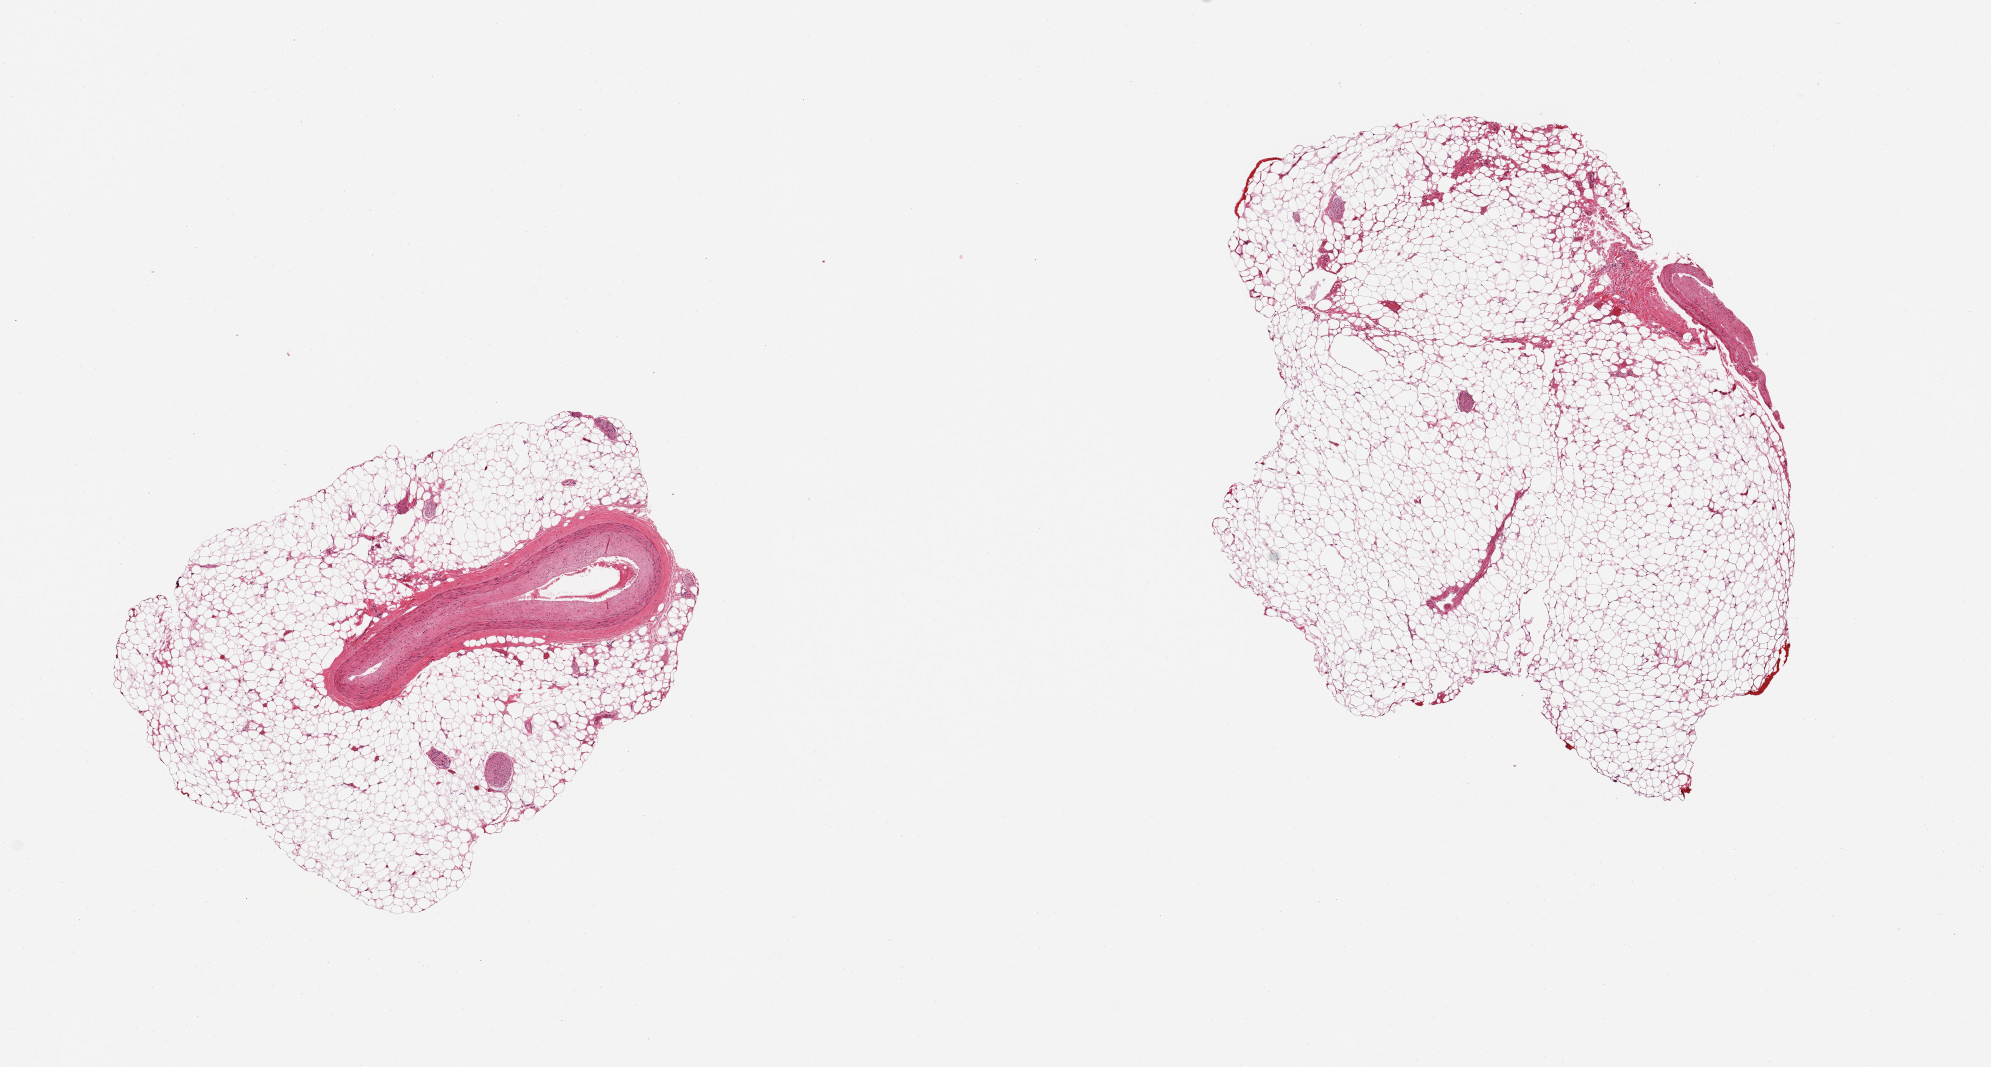
Whole-slide image, haematoxylin and eosin stain, whole scanned area (about 15.8 x 8.4 mm) shown as a low-resolution overview, PAXgene-fixed, paraffin-embedded tissue, section of coronary artery (target tissue), donor tissue sample. Donor sex: male.
Reviewer comment on this tissue sample: 2 pieces; 1 piece is 75% external fat; other is 95% external fat.